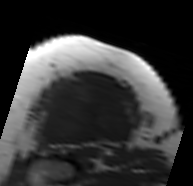
MRI of an extremity soft-tissue mass, one axial slice. Slice 58 of 91 in the series (ordered by position). MR volume resampled by the dataset authors to the PET/CT grid (not the native acquisition matrix). 3.27 mm slice thickness. 193 × 186 image matrix, field of view 188 × 182 mm. Female patient. From the clinical record (not read from this slice): histological type: malignant solitary fibrous tumor; grade: intermediate; site of the primary tumour: right thigh.
Outlined on this slice (expert contour drawn on MRI and transferred to this co-registered scan by the dataset authors):
- gross tumour volume including surrounding oedema: bounding box <35,78,135,148> (left, top, right, bottom; pixels)
- gross tumour volume (mass): <35,81,132,148>